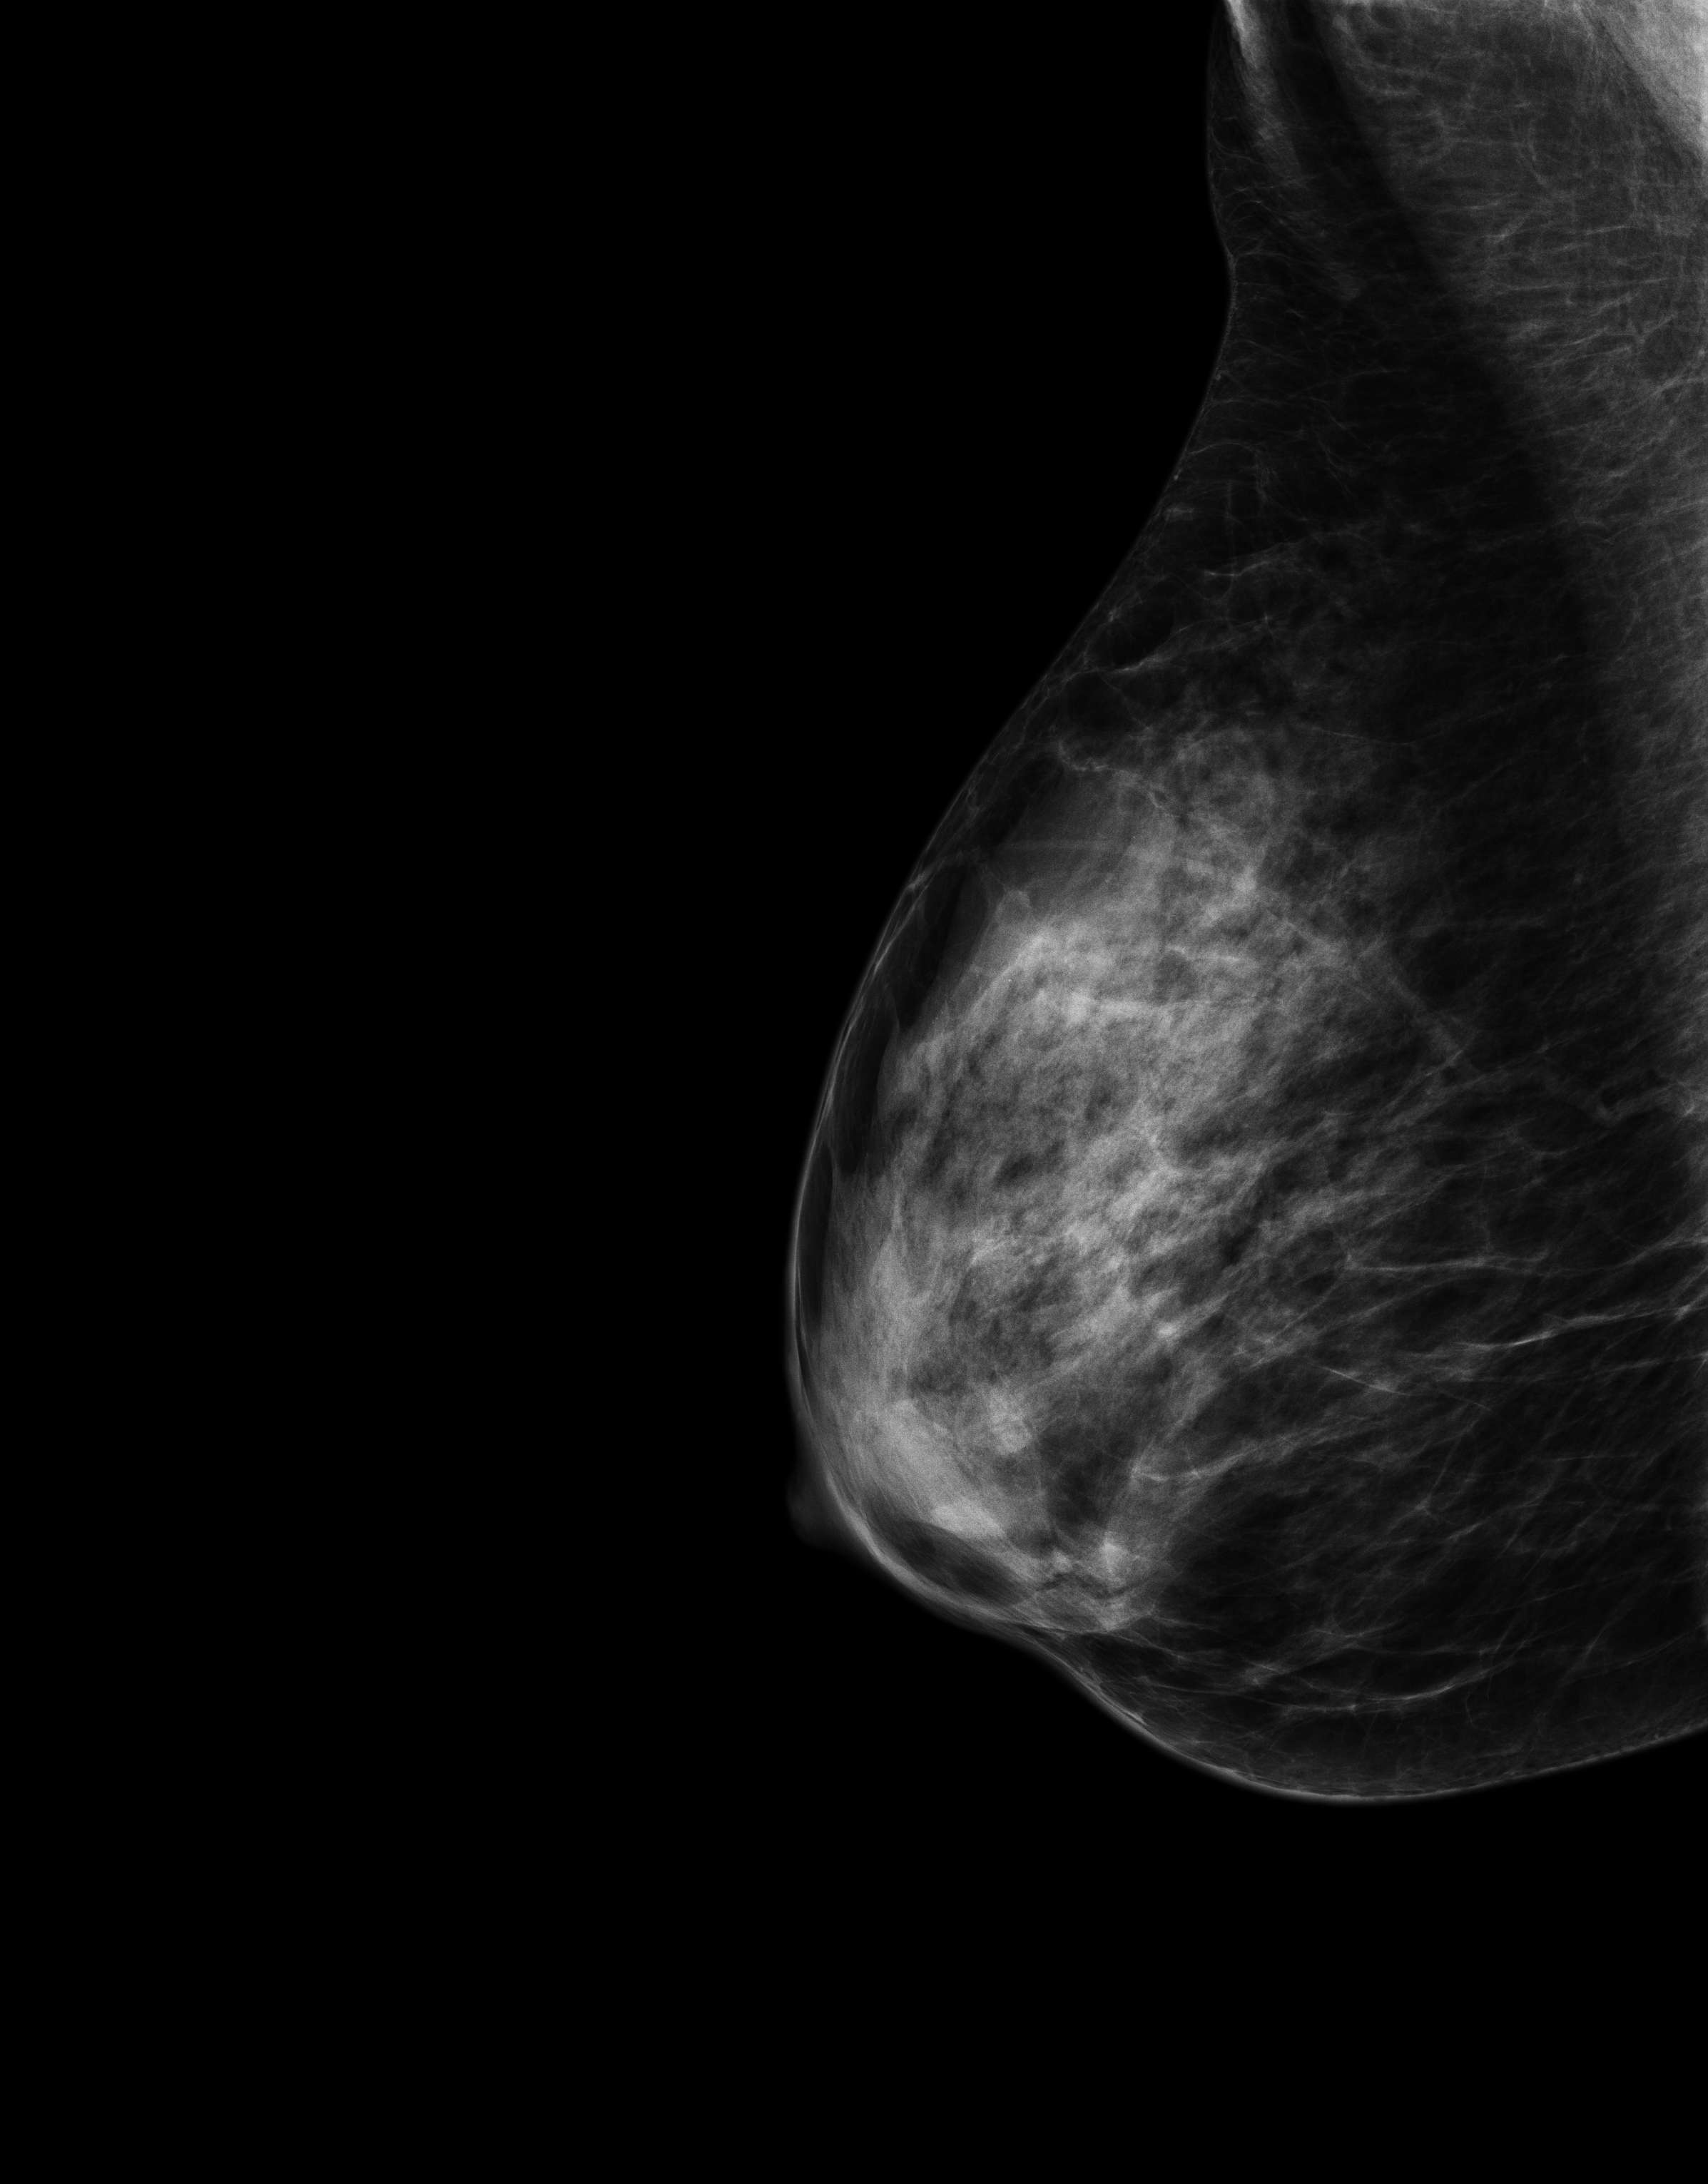
Screening examination, compressed breast thickness 41 mm. Patient: female, 49 years.
Image type: full-field digital mammogram. Breast: right. Projection: MLO view.